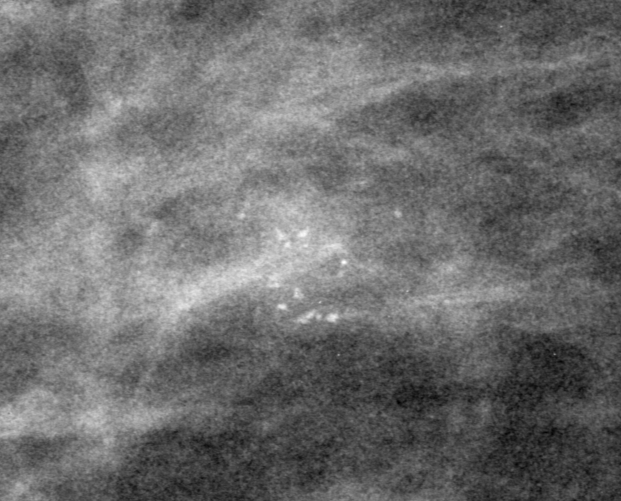
Cropped region of a digitized screen-film mammogram centred on a radiologist-marked abnormality, right breast, MLO view, BI-RADS breast density category 2 (scale 1–4).
- Calcifications, morphology pleomorphic, distribution clustered; BI-RADS assessment category 0 (incomplete: needs additional imaging); subtlety rating 5 on a 1 (subtle) to 5 (obvious) scale; pathology result (as recorded, not read from the image): benign.